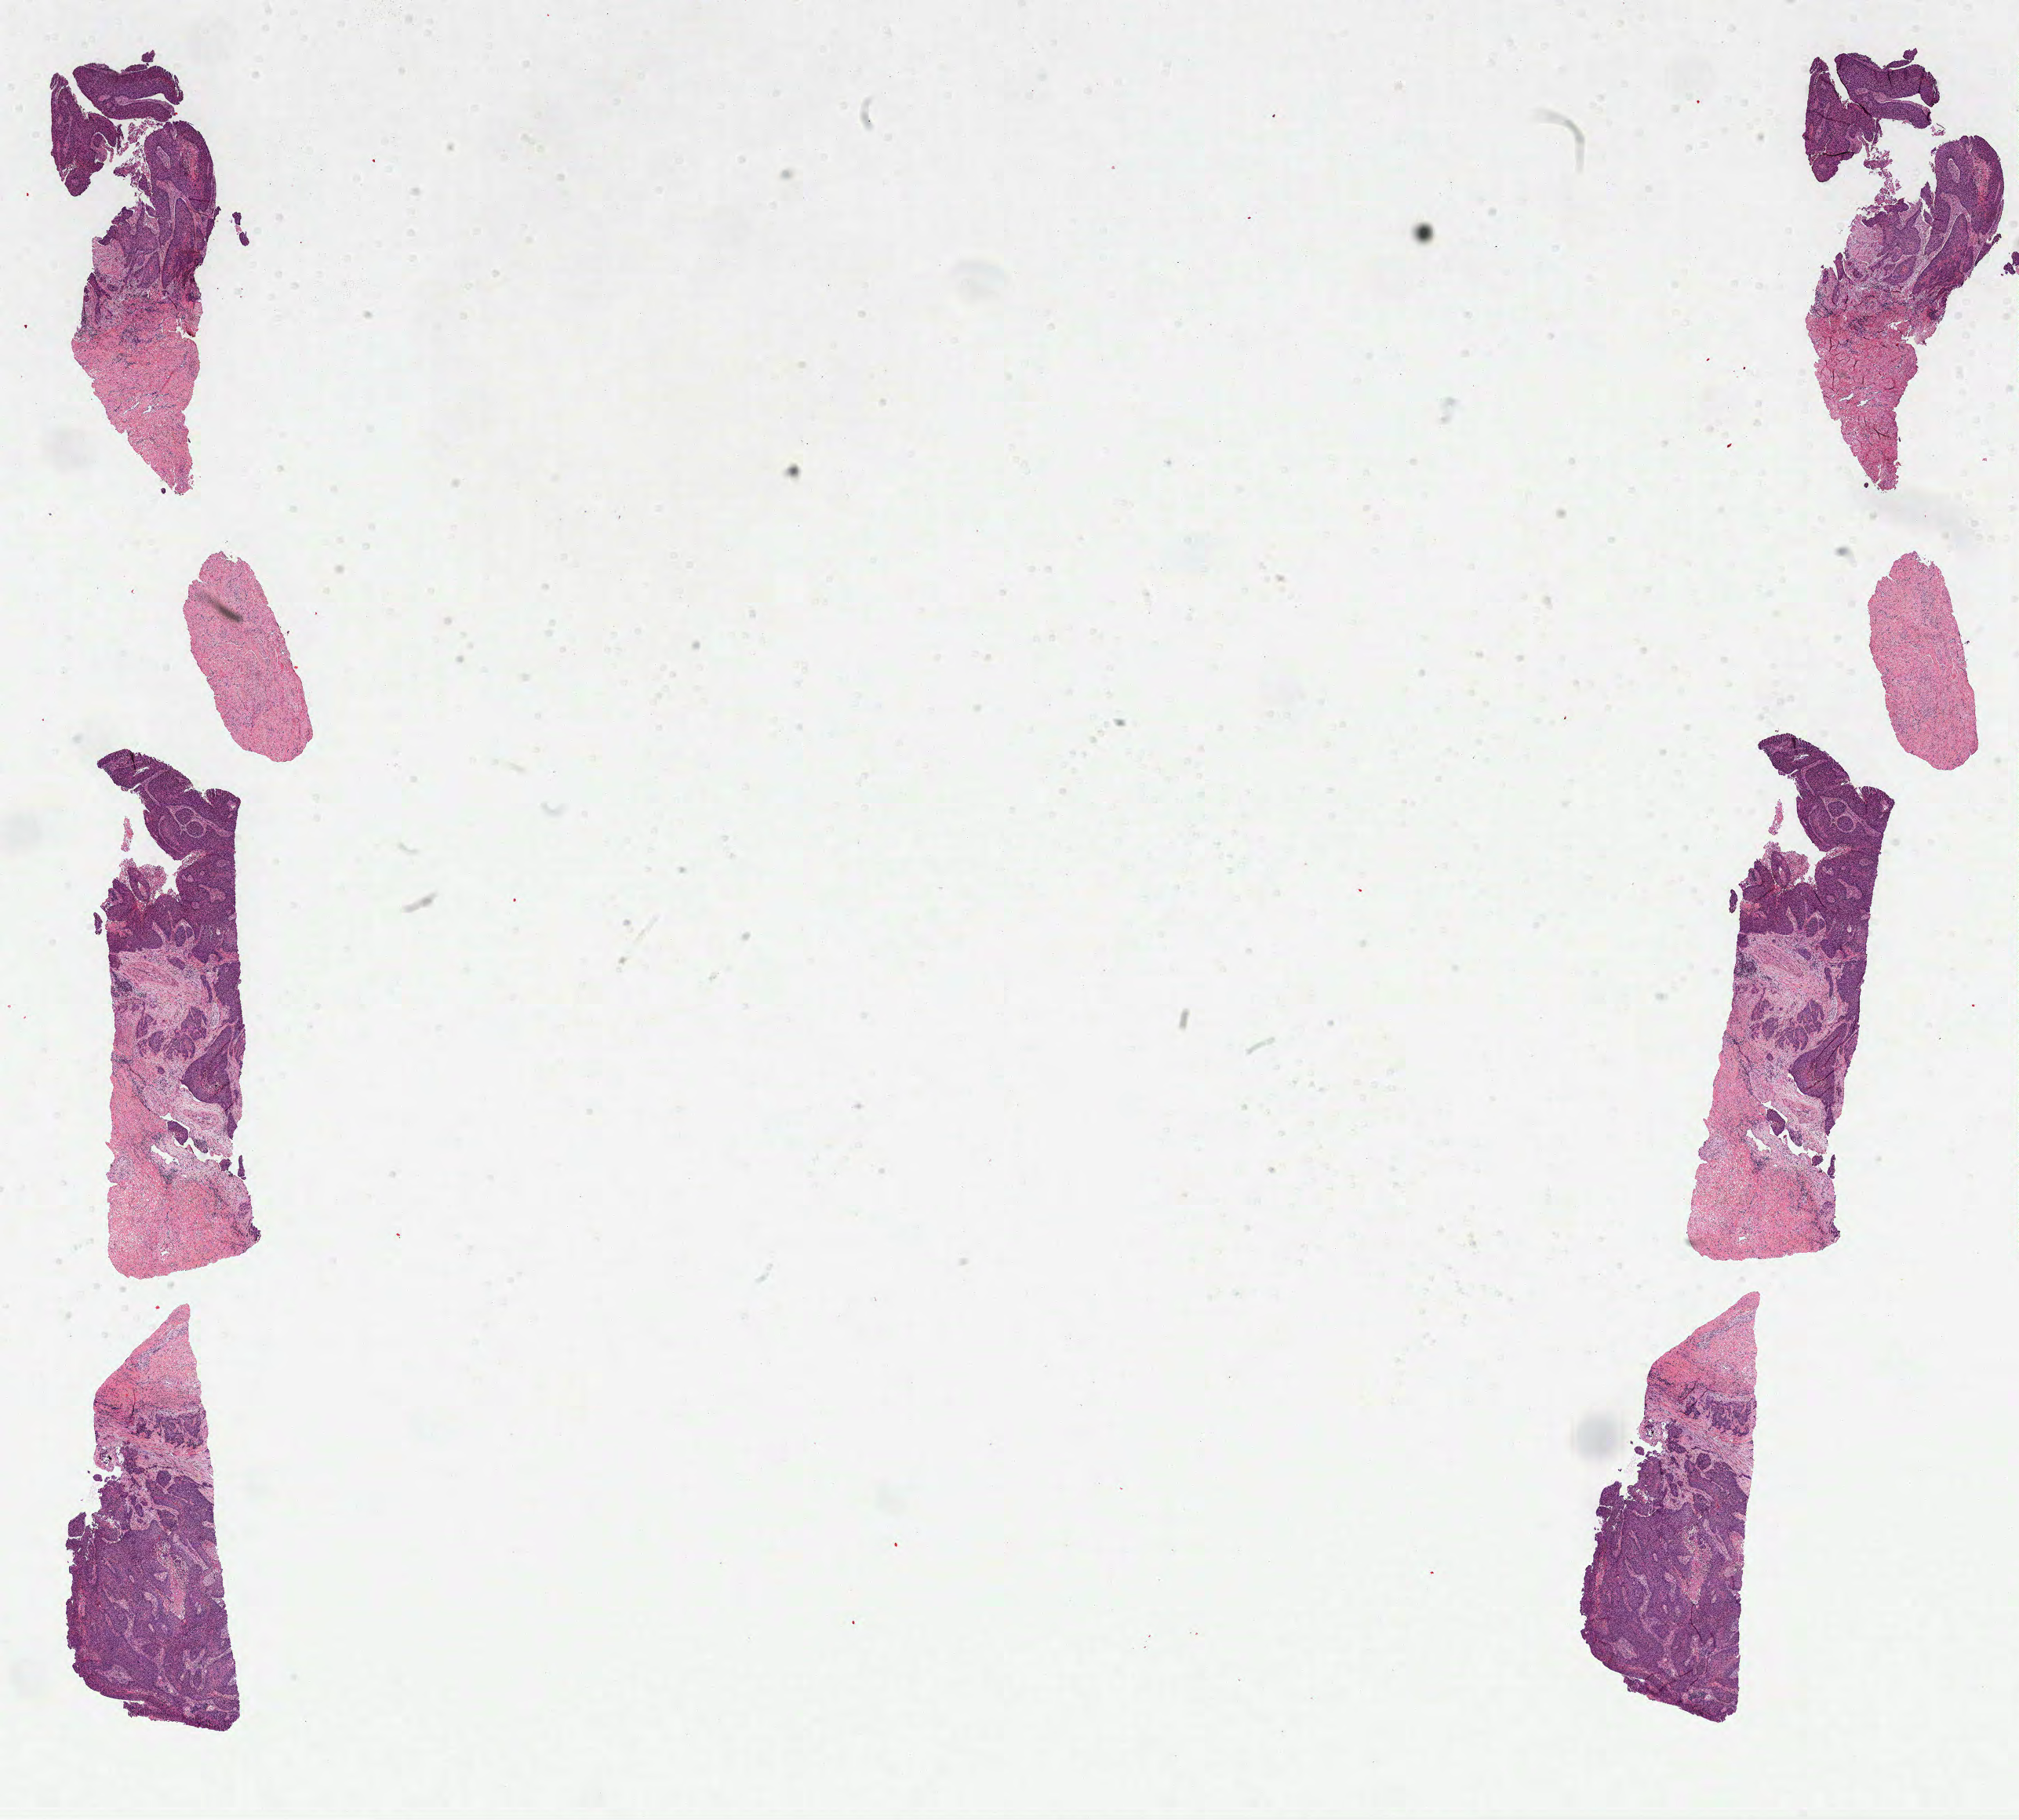
H&E-stained whole-slide image, a low-resolution overview of the entire scanned area, about 20.7 x 18.7 mm (acquisition: 40x scan); FFPE section; sample: primary tumour, cervix. Patient: female, age at initial diagnosis 43 years.
* diagnosis: Squamous cell carcinoma, keratinizing, NOS (cervix uteri)
* FIGO stage: IIB